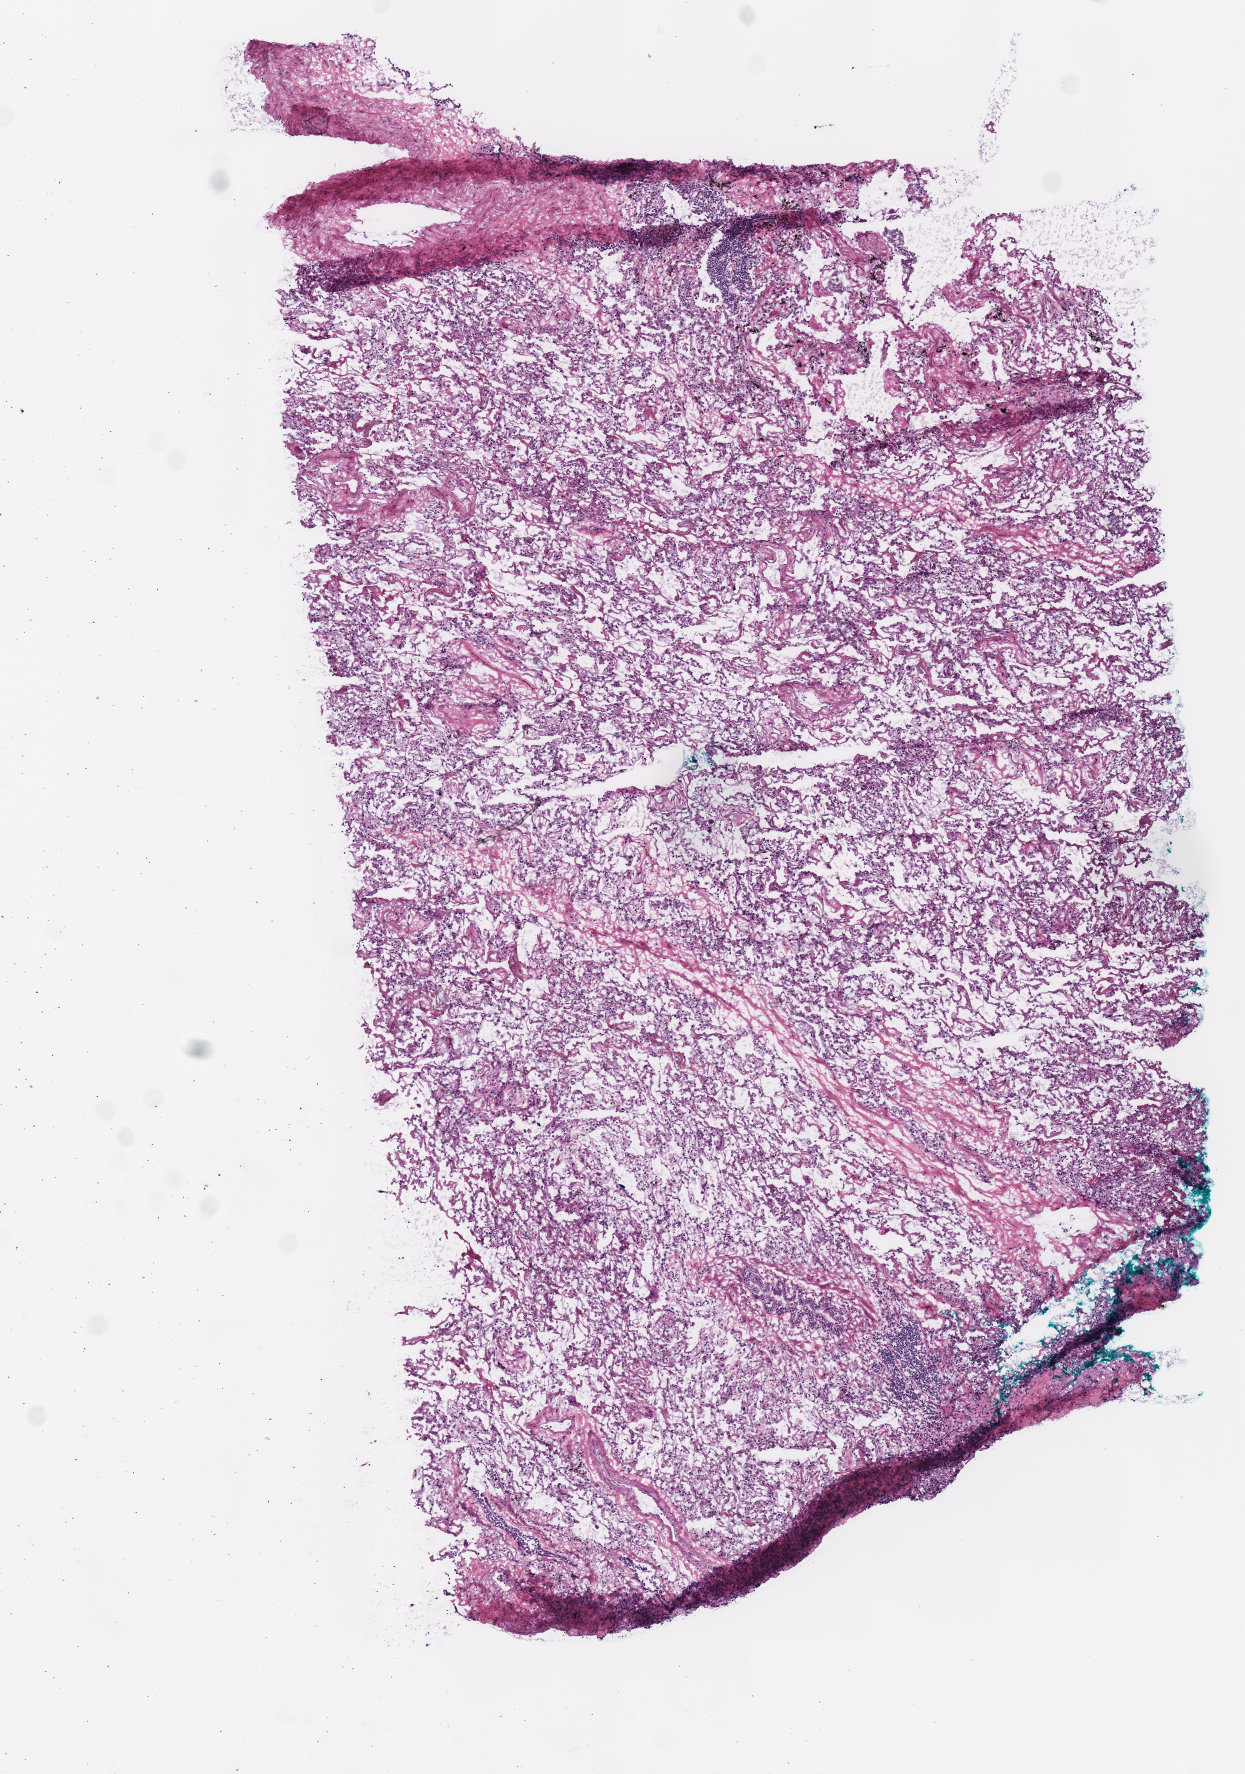
Digitized Hematoxylin and eosin (H&E) stained tissue section (whole slide) — whole scanned area (about 4.9 x 7.0 mm) shown as a low-resolution overview, frozen section, lung, solid tissue normal (non-tumour tissue) sample. Male patient; age at initial diagnosis 72 years.
* this section: solid tissue normal sample (biorepository sample class)
* patient diagnosis: Squamous cell carcinoma, NOS (upper lobe, lung)